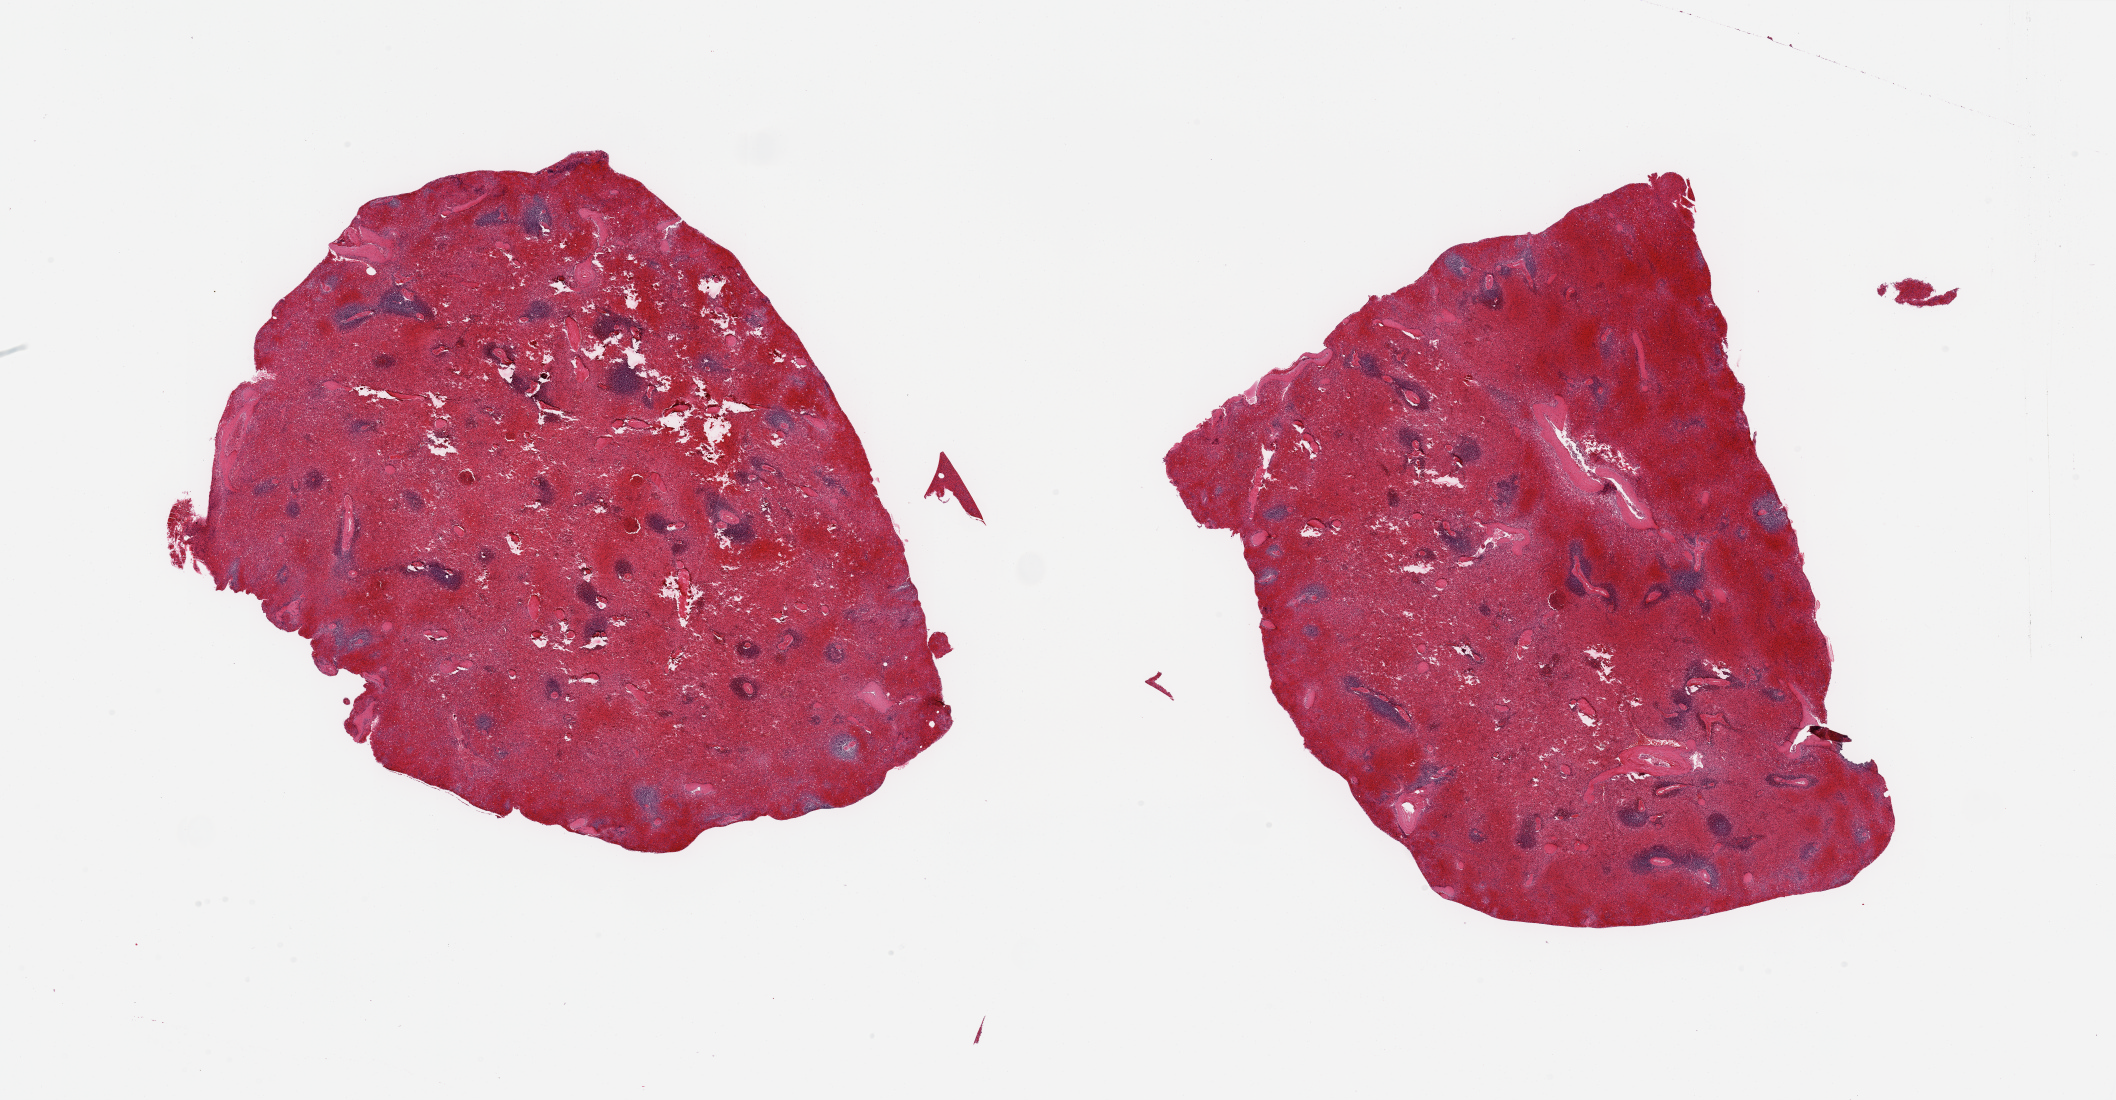
Digitized haematoxylin and eosin-stained section — whole scanned area (about 33.5 x 17.4 mm, acquisition: 20x scan) shown as a low-resolution overview. PAXgene-fixed paraffin-embedded (PFPE) section. Sampled site (target tissue): spleen. Donor tissue sample. Donor: male.
Review note (as recorded): 2 pieces; mild to moderate autolysis; marked congestion.